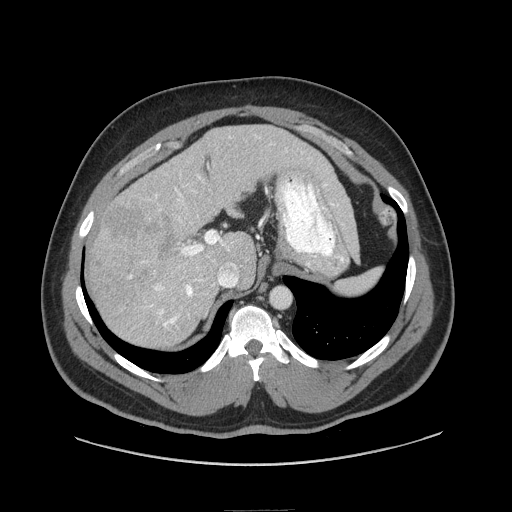
Contrast-enhanced abdominal CT (liver protocol), one axial slice. Slice 55 of 87 in the series (ordered by position). 140 kVp. Soft-tissue window (W 400 / L 40 HU). 2.5 mm slice thickness. 512 × 512 image matrix, field of view 440 × 440 mm. From the clinical record (not read from this slice): diagnosis: hepatocellular carcinoma (patient treated with transarterial chemoembolisation; whether this scan precedes or follows treatment is not stated here); TNM stage (as recorded): Stage-II; Child-Pugh class: A; tumour differentiation: moderately differentiated; tumour nodularity: uninodular.
Structures marked on this image (semi-automatically segmented with operator editing):
- liver parenchyma outside the tumour (the mass and vessels are separate outlines, so this box may not span the whole liver): bounding box [x1, y1, x2, y2] px = [88, 126, 333, 346]
- mass: [101, 201, 182, 271]
- liver vessels: [129, 176, 236, 327]